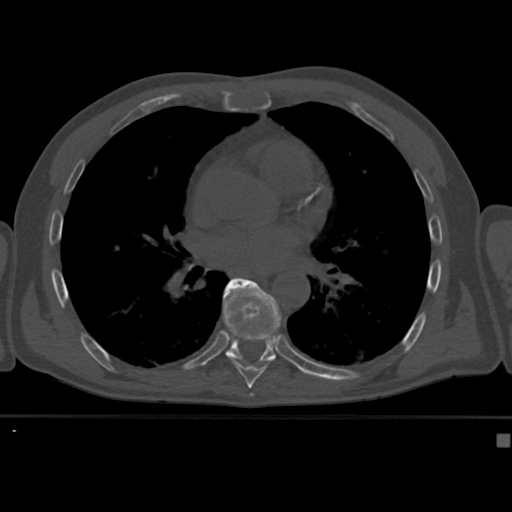
CT including the spine, one axial slice; position 256 of 430 along the scan axis; reconstruction kernel Br40s; 120 kVp; bone window (W 1800 / L 400 HU); 512 × 512 image matrix, field of view 337 × 337 mm. Male patient, age 64 years. Case-level facts recorded for this patient, not image findings: primary cancer: uterus; vertebrae with lytic lesions (as recorded): T1, T4, T5, T7, L5.
Annotated regions visible in this slice (semi-automatic segmentation, software-assisted and operator-edited):
- T8 vertebra: box from (x=220, y=282) to (x=281, y=382) px
- T9 vertebra: (x=223, y=277)–(x=283, y=374)